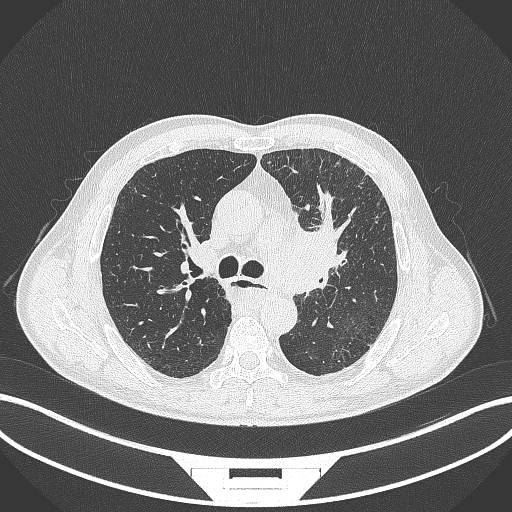
Chest CT, one axial slice; slice 246 of 411 in the series (ordered by position); reconstruction kernel B70f; lung window (W 1500 / L -600 HU); 1 mm slice thickness; 512 × 512 image matrix. Male patient, age 57 years. From the clinical record (not read from this slice): clinical TNM (as recorded): T2a N1 M0.
Structures marked on this image (bounding box drawn by a radiologist):
- lung tumour (recorded histology: squamous cell carcinoma): bounding box [x1, y1, x2, y2] px = [265, 221, 349, 298]